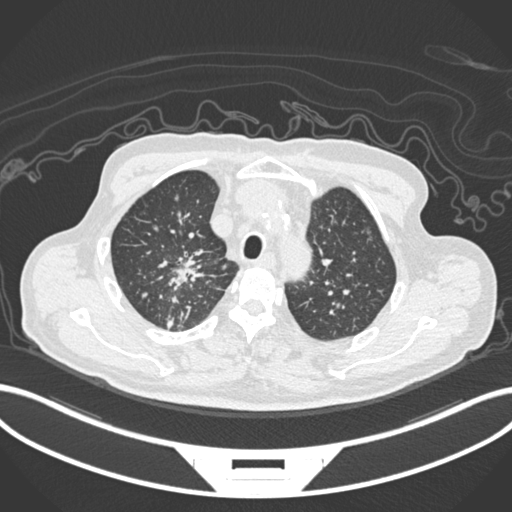
Chest CT, one axial slice. Position 169 of 207 along the scan axis. Reconstruction kernel B30f. 120 kVp. Lung window (W 1500 / L -600 HU). 1 mm slice thickness. 512 × 512 image matrix. Patient: male, 69 years. From the clinical record (not read from this slice): clinical TNM (as recorded): T1c N1 M1.
Outlined on this slice (bounding box drawn by a radiologist):
- lung tumour (recorded histology: adenocarcinoma): bounding box [x1, y1, x2, y2] px = [162, 250, 215, 299]